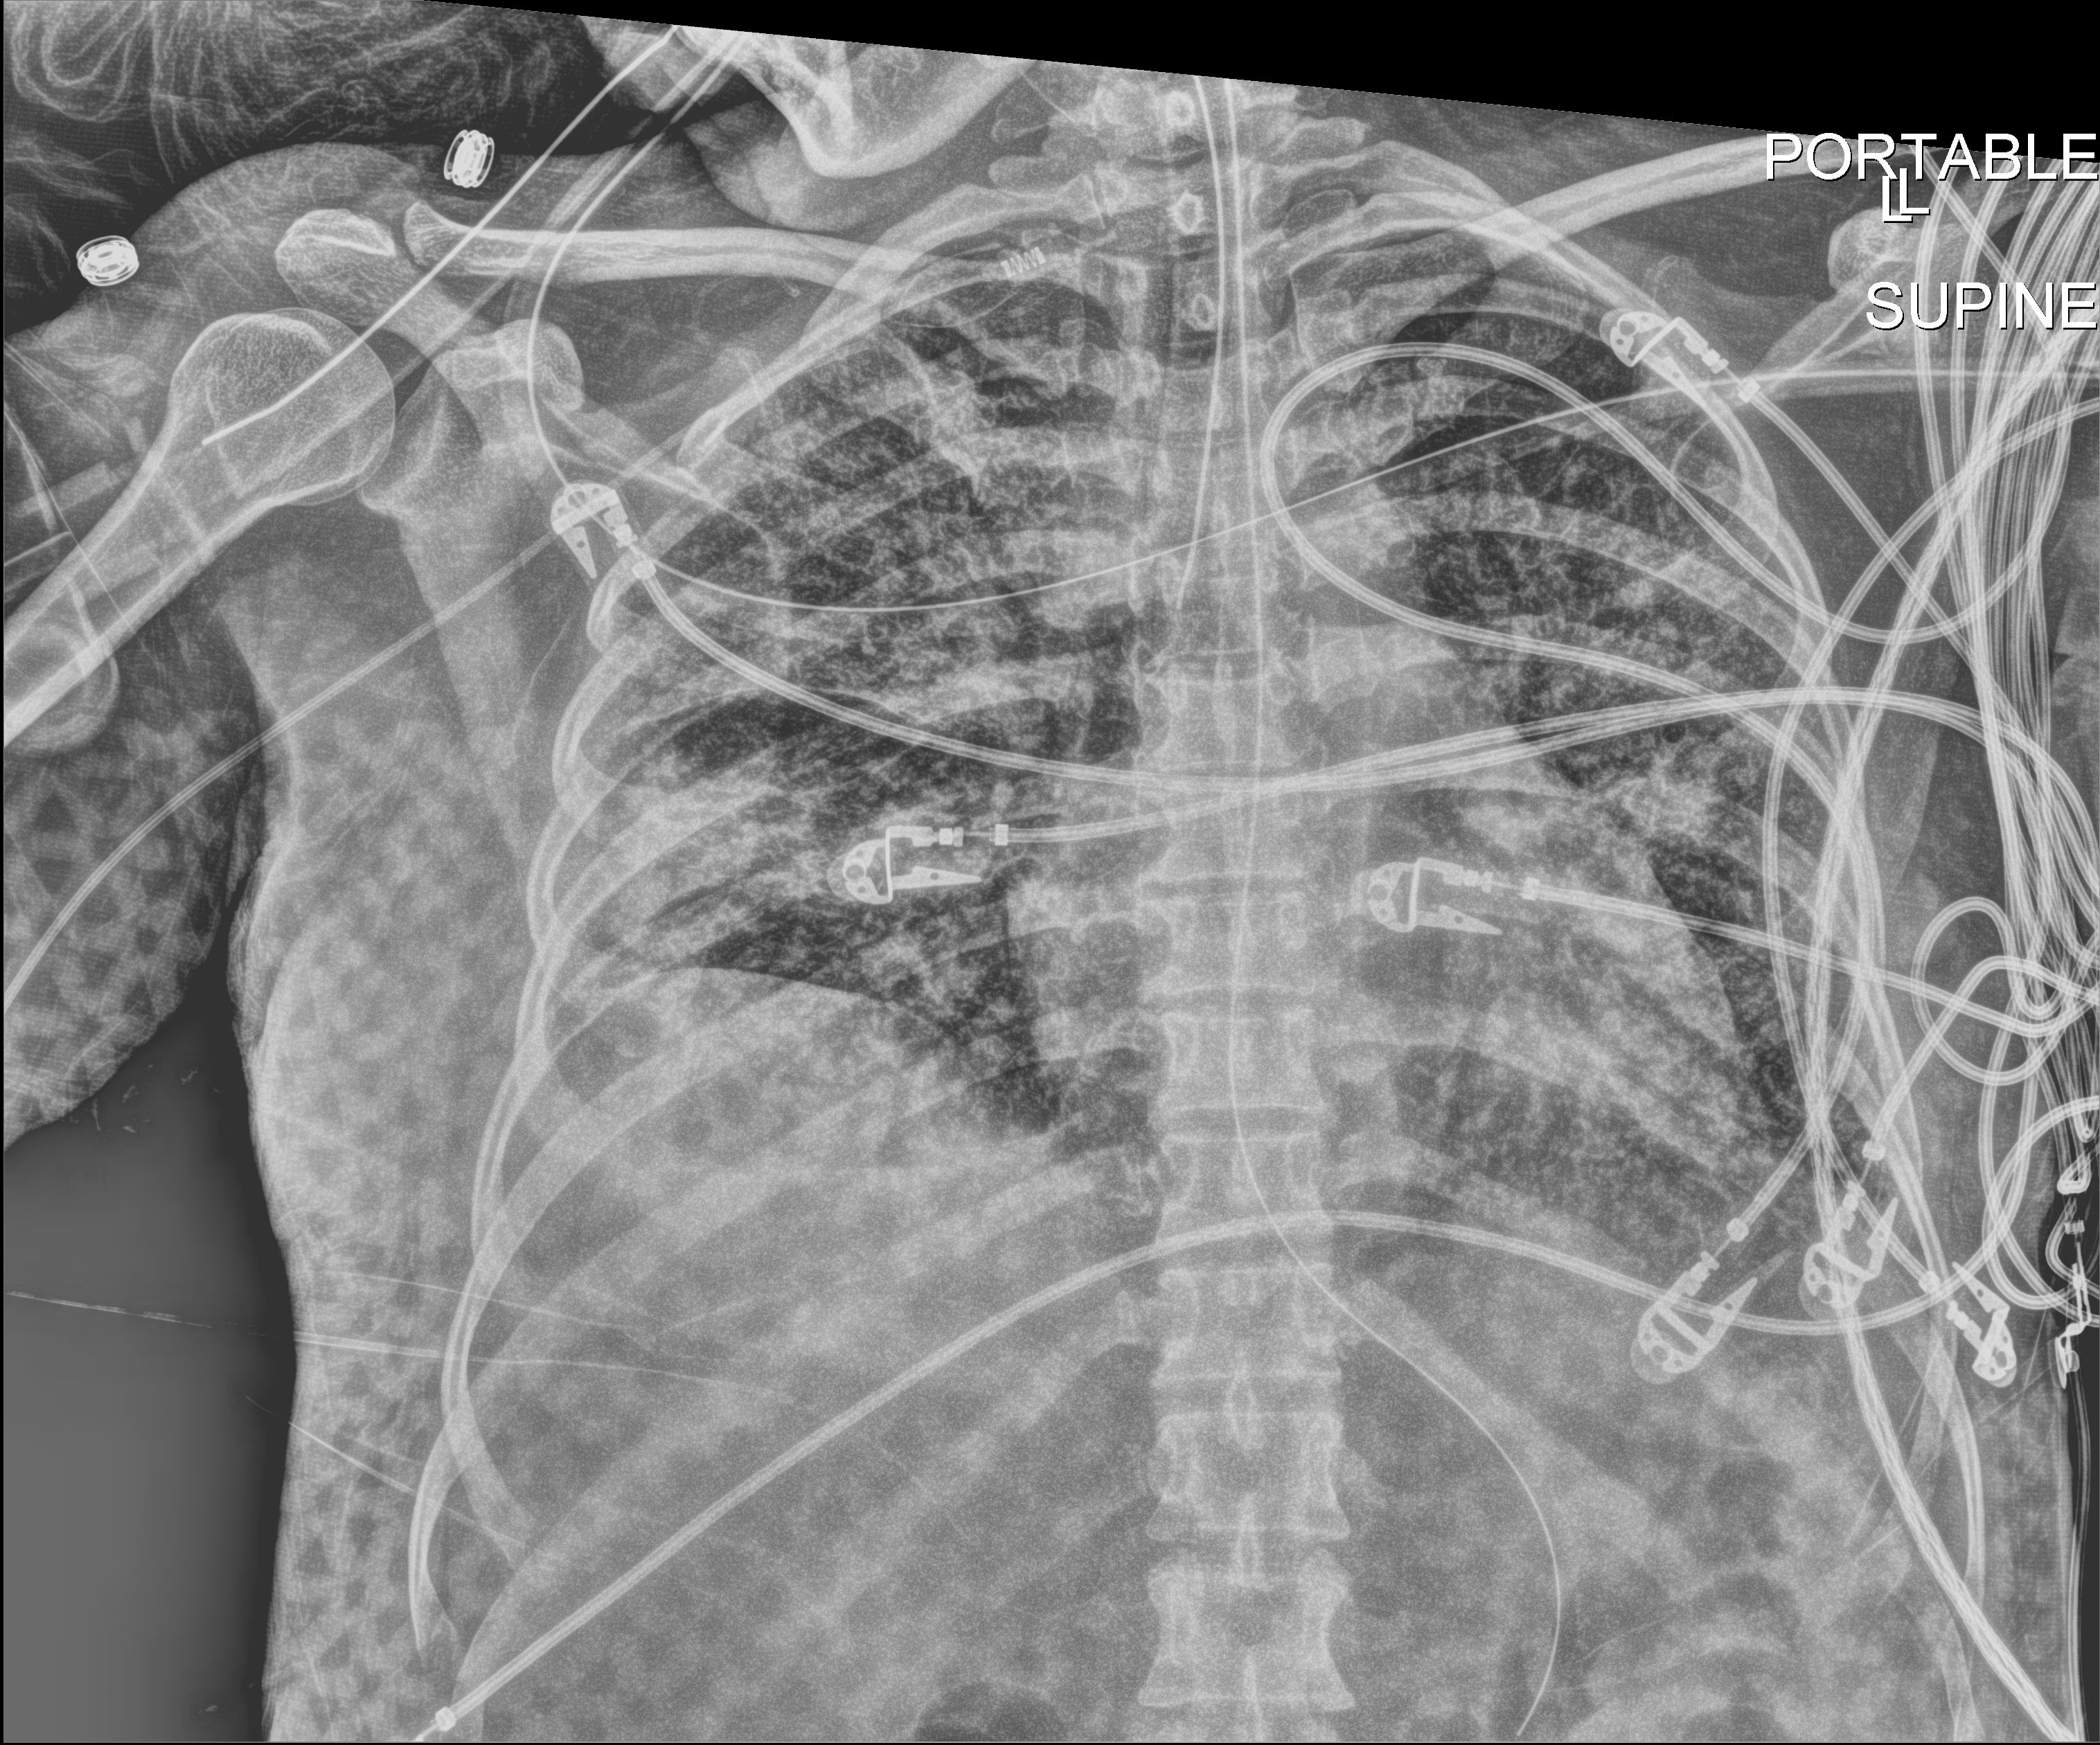
Chest X-ray (portable); anteroposterior (AP) projection. Patient hospitalised with COVID-19; female, aged 18–59 years.
From the hospital-stay record, not from the radiograph (when in the stay this image was taken is not recorded): mechanically ventilated during this hospital stay: yes; admitted to intensive care during this hospital stay: yes.